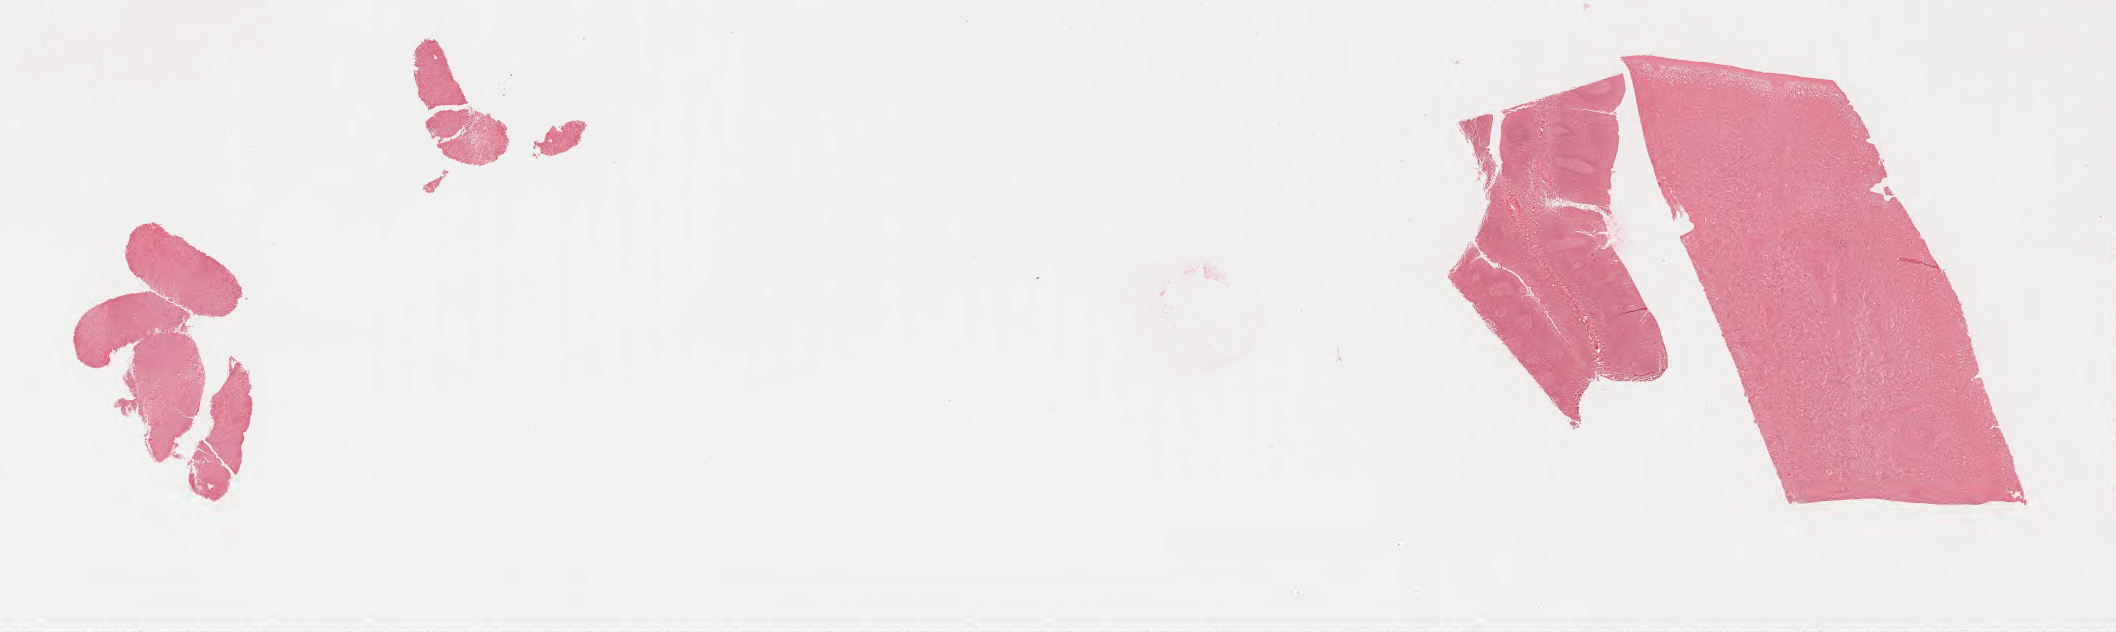
In-situ hybridisation whole-slide image, Epstein–Barr virus-encoded RNA (EBER) probe, whole scanned area (about 34.2 x 10.2 mm) shown as a low-resolution overview. Specimen: tumor tissue. Site: lymph node. Patient: male, 54 years old.
* histologic diagnosis: Diffuse large B-cell lymphoma, NOS